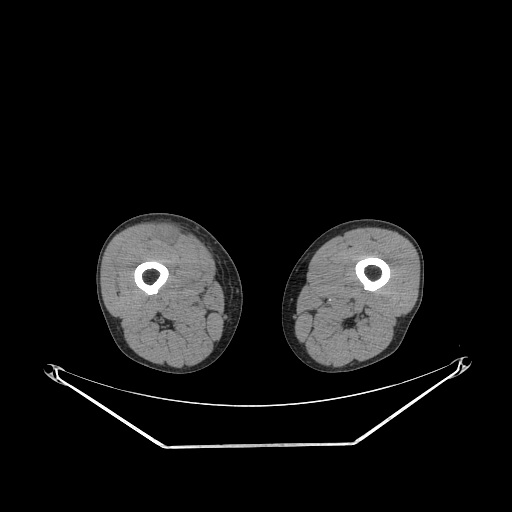
CT of an extremity soft-tissue mass (from a PET/CT study), one axial slice; reconstruction kernel STANDARD; 140 kVp; soft-tissue window (W 400 / L 40 HU); 512 × 512 image matrix, field of view 500 × 500 mm. Male patient. From the clinical record (not read from this slice): histological type: pleiomorphic leiomyosarcoma; grade: intermediate; site of the primary tumour: right thigh.
Outlined on this slice (expert contour drawn on MRI and transferred to this co-registered scan by the dataset authors):
- gross tumour volume including surrounding oedema: bounding box <157,228,181,245> (left, top, right, bottom; pixels)